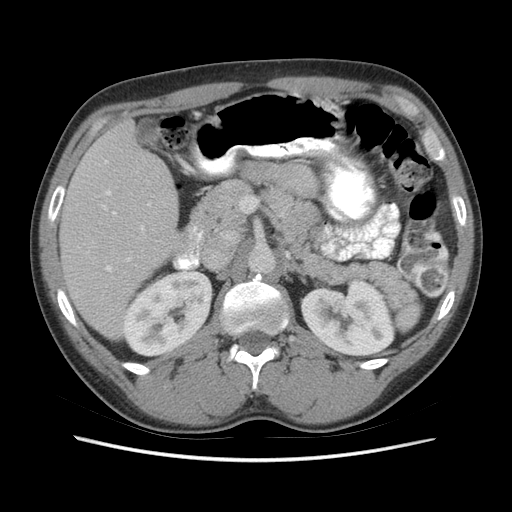
Contrast-enhanced abdominal CT (liver protocol), one axial slice; position 29 of 73 along the scan axis; soft-tissue window (W 400 / L 40 HU); 2.5 mm slice thickness; 512 × 512 image matrix, field of view 360 × 360 mm. Case-level facts recorded for this patient, not image findings: diagnosis: hepatocellular carcinoma (patient treated with transarterial chemoembolisation; whether this scan precedes or follows treatment is not stated here); TNM stage (as recorded): Stage-IIIA; Child-Pugh class: A; tumour nodularity: multinodular; tumour size: 6.6 cm.
Annotated regions visible in this slice (semi-automatic segmentation, software-assisted and operator-edited):
- liver parenchyma outside the tumour (the mass and vessels are separate outlines, so this box may not span the whole liver): bounding box [x1, y1, x2, y2] px = [60, 122, 194, 336]
- liver vessels: [103, 161, 150, 272]